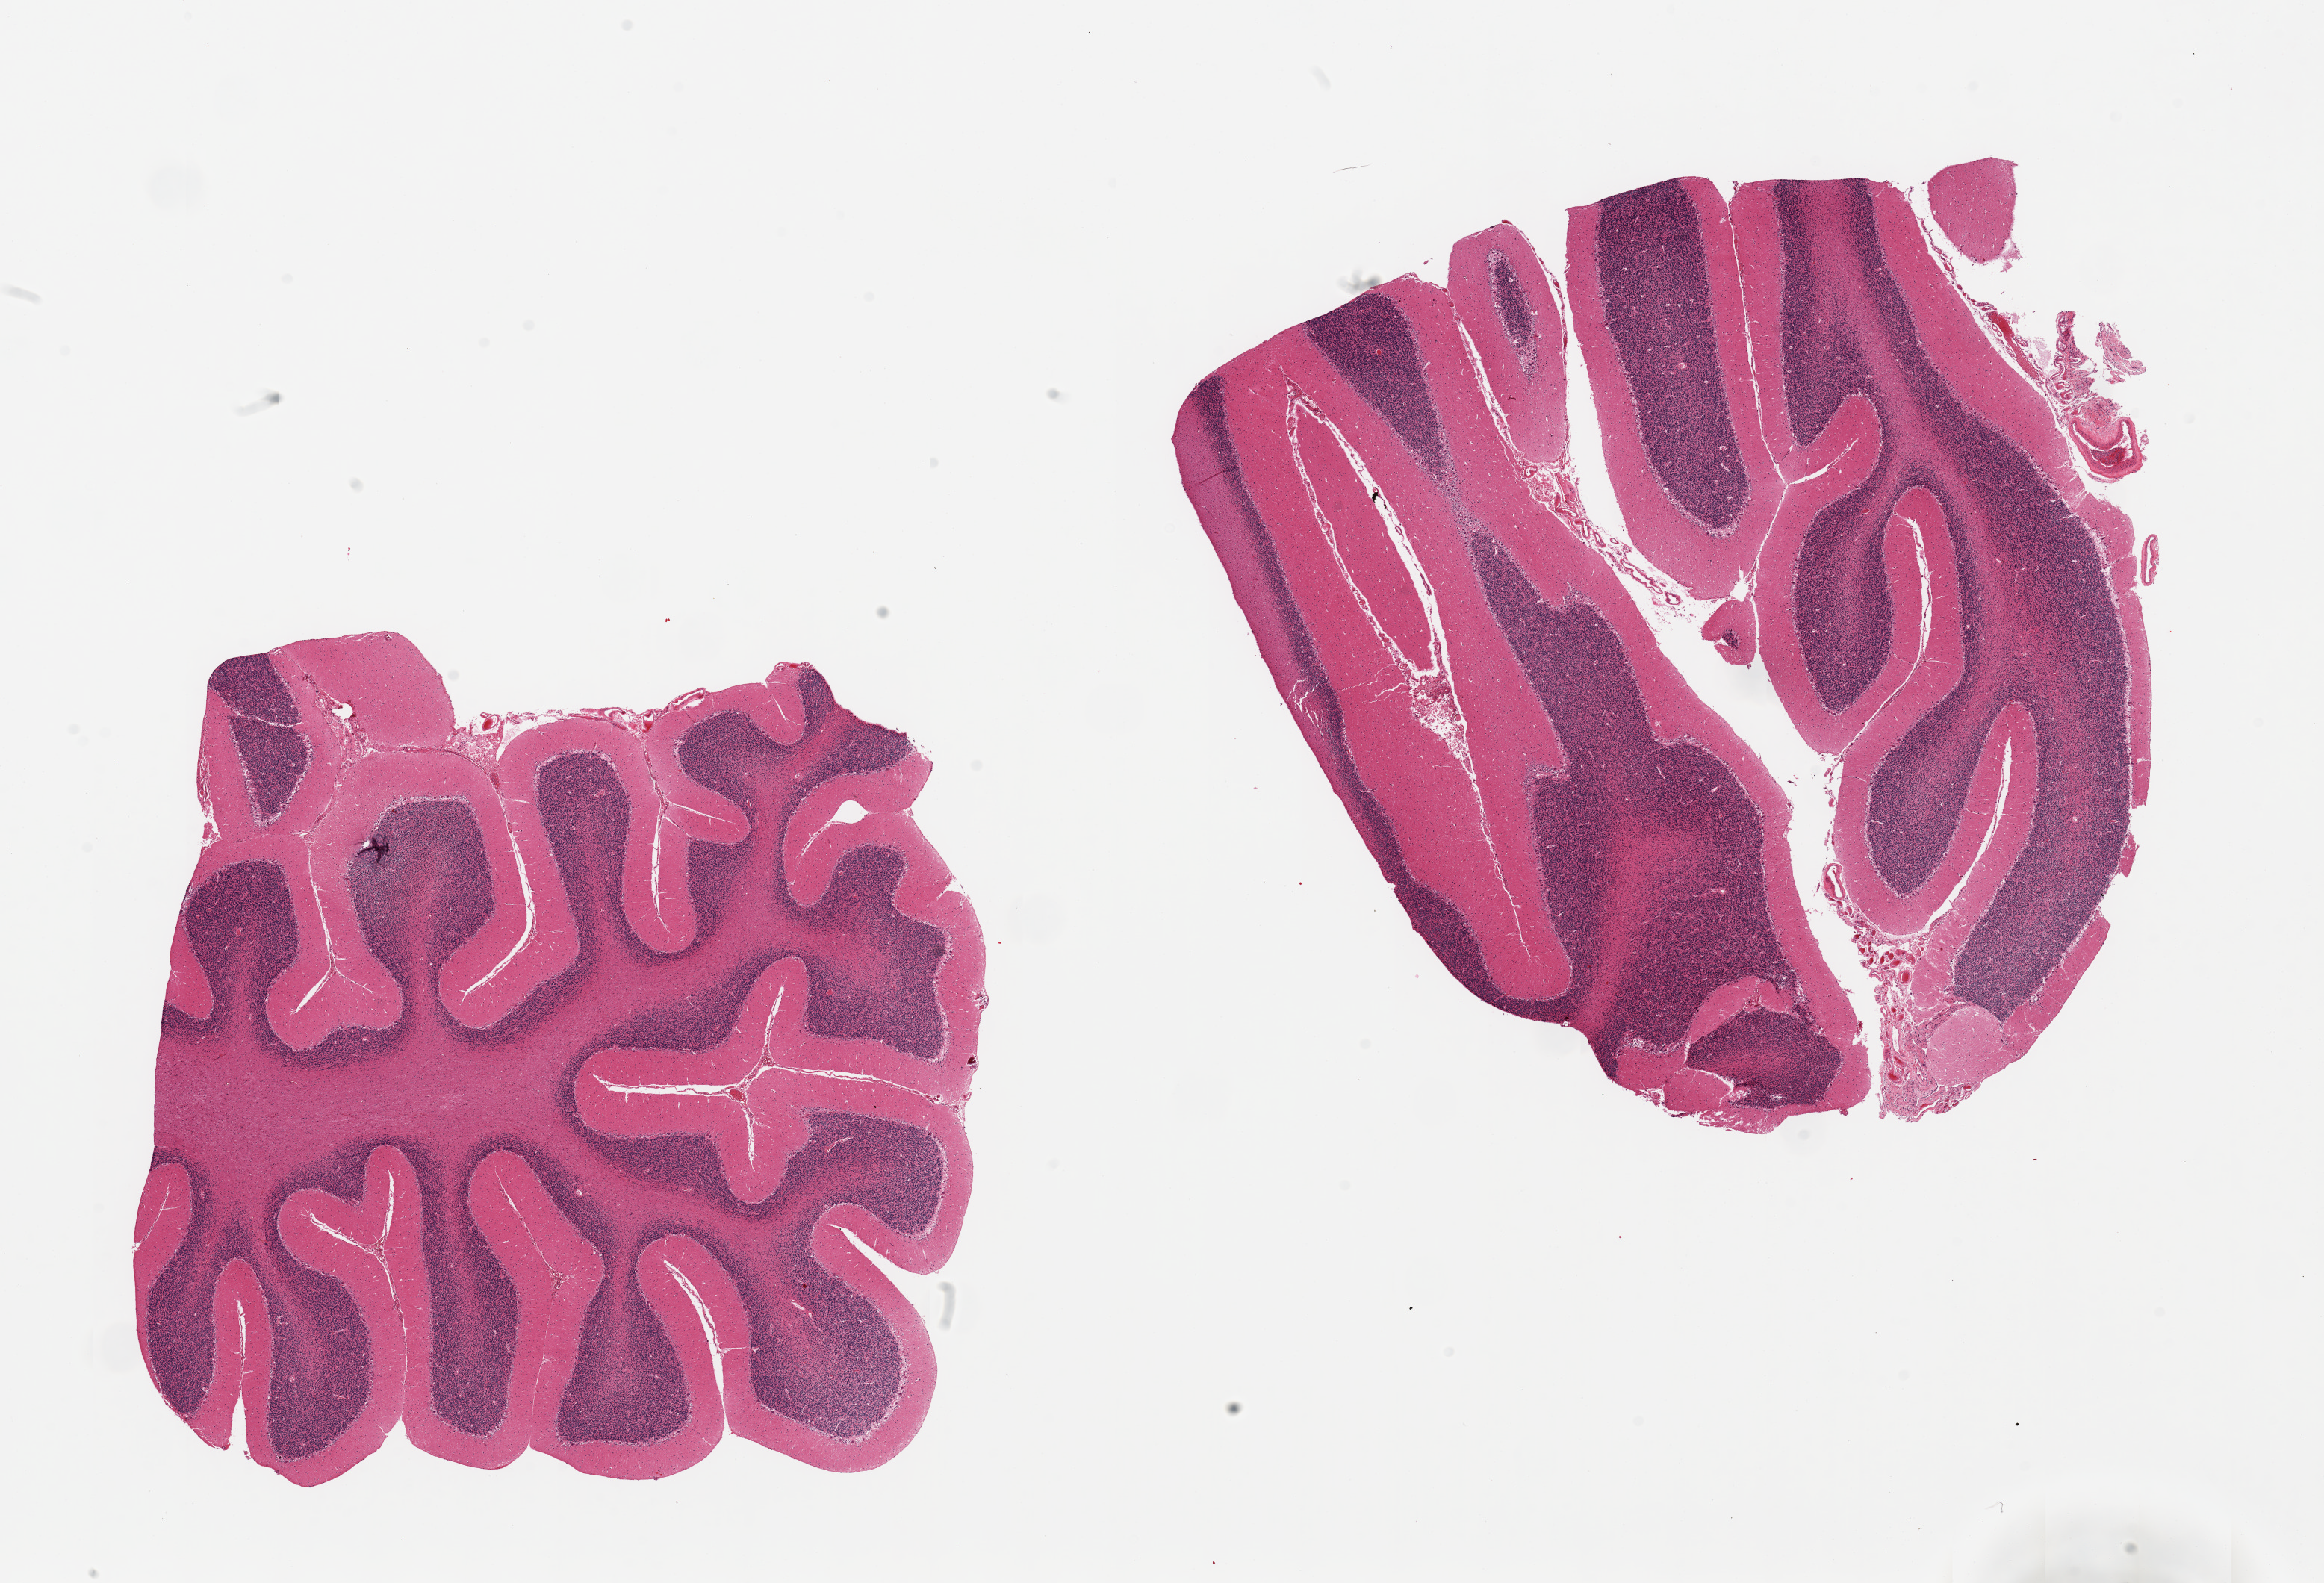
Digitized hematoxylin and eosin (H&E)-stained section, brightfield, whole scanned area (about 24.6 x 16.8 mm, from a 20x scan) shown as a low-resolution overview; PAXgene-fixed paraffin-embedded (PFPE) section; sampled site (target tissue): cerebellum; tissue donor sample.
Pathologist's review note for this sample: 2 pieces, no abnormalities.